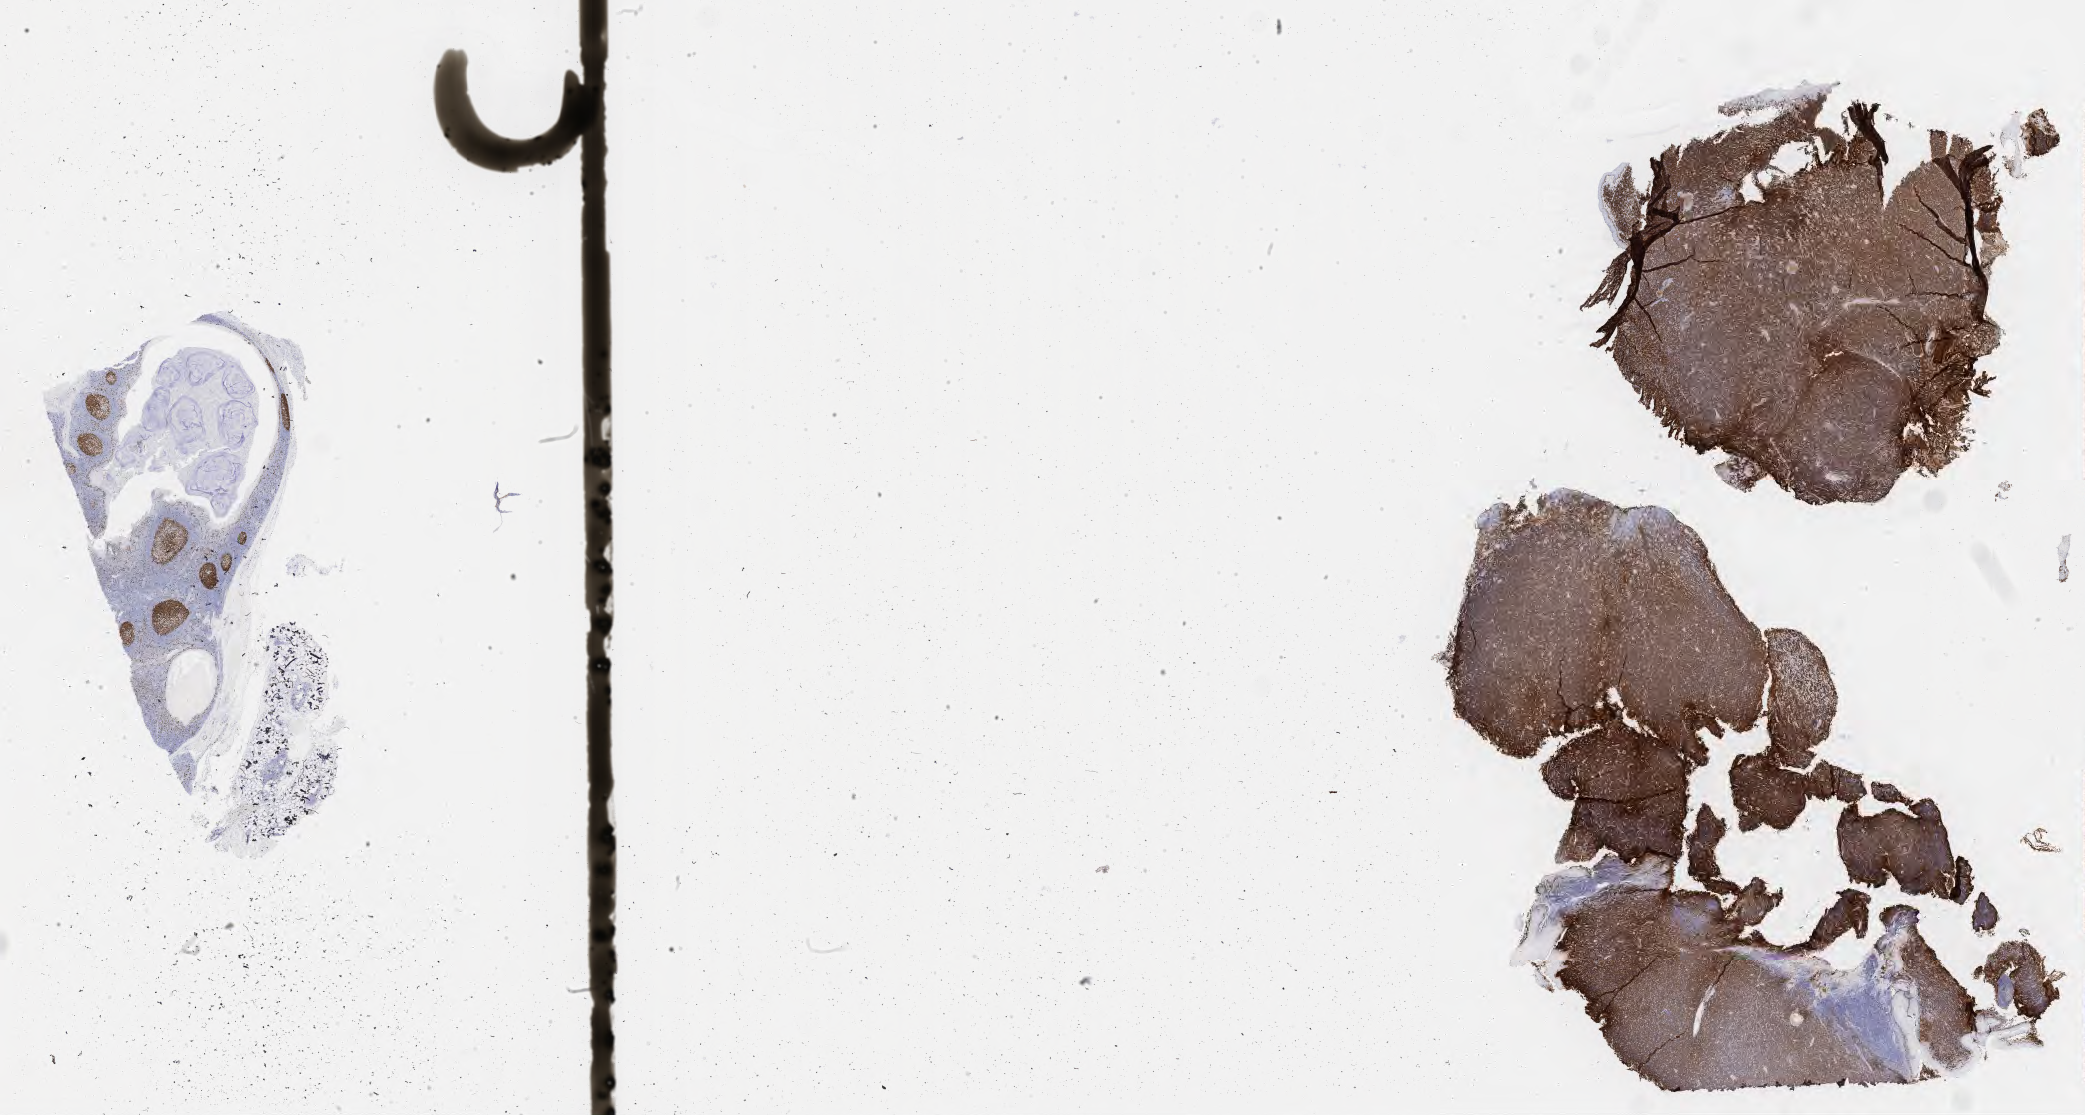
IHC for Ki-67, whole-slide image — a low-resolution overview of the entire scanned area, about 33.7 x 18.0 mm; specimen: tumor tissue. Patient: male, 22 years old.
Diagnosis: Diffuse large B-cell lymphoma, NOS.